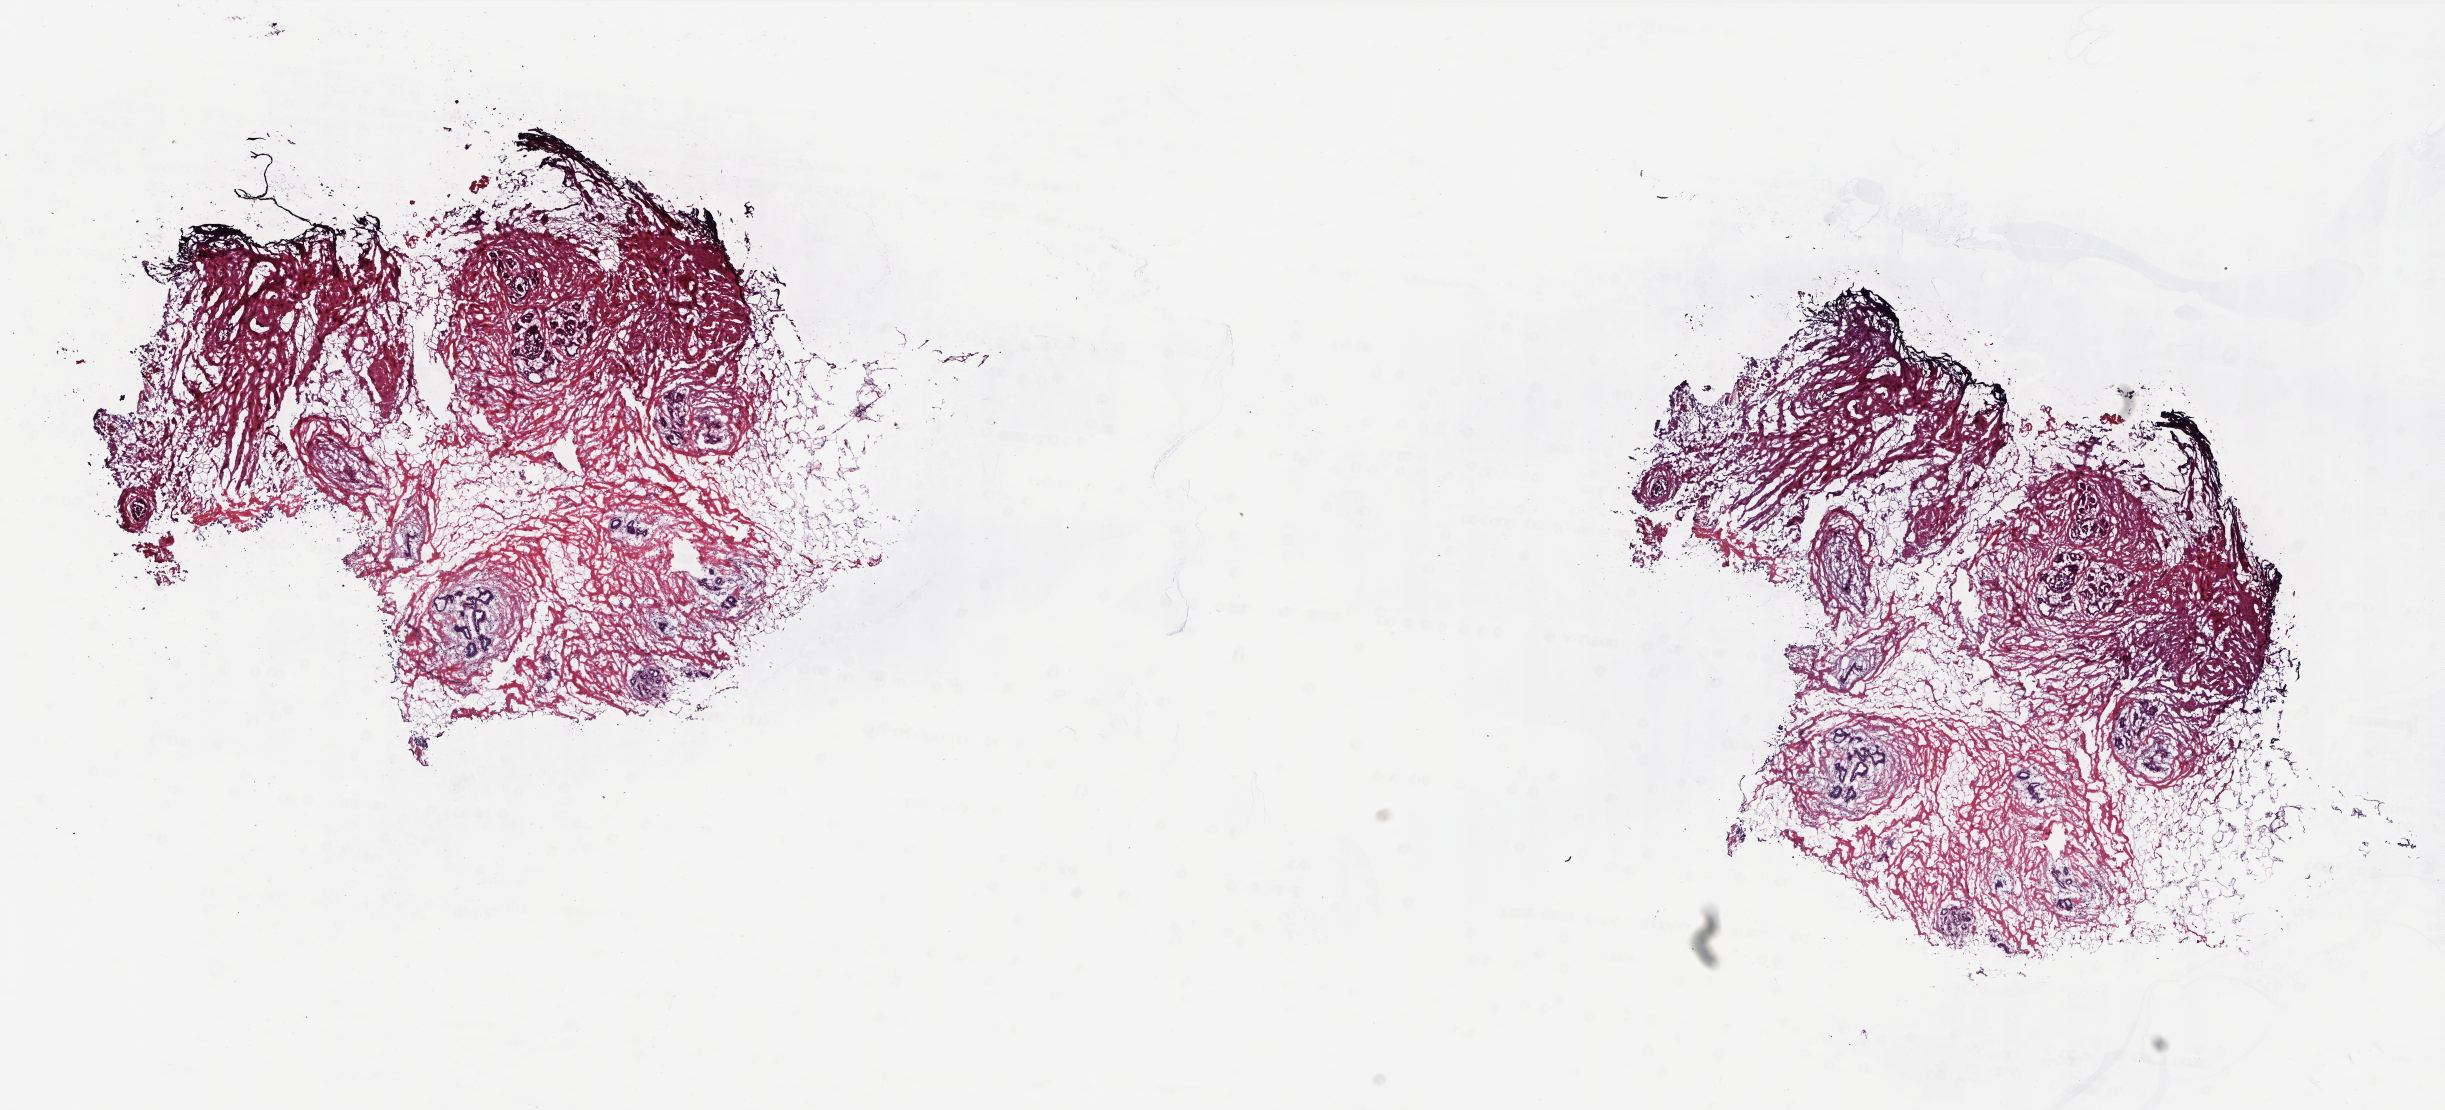
Whole-slide histology image, H&E, shown as a low-resolution overview of the whole scanned area (about 19.7 x 9.0 mm, acquisition: 20x scan), frozen section, skin, solid tissue normal (non-tumour tissue) sample. Patient: female, age at initial diagnosis 48 years. Composition of this section per pathologist review: tumour cells 0%, tumour nuclei 0%, normal cells 10%, stromal cells 90%, necrosis 0%. Infiltration values recorded for this section: lymphocyte infiltration 2%, monocyte infiltration 1%, neutrophil infiltration 1%.
* this section: solid tissue normal (non-tumour) sample from the same patient
* patient diagnosis: Malignant melanoma, NOS